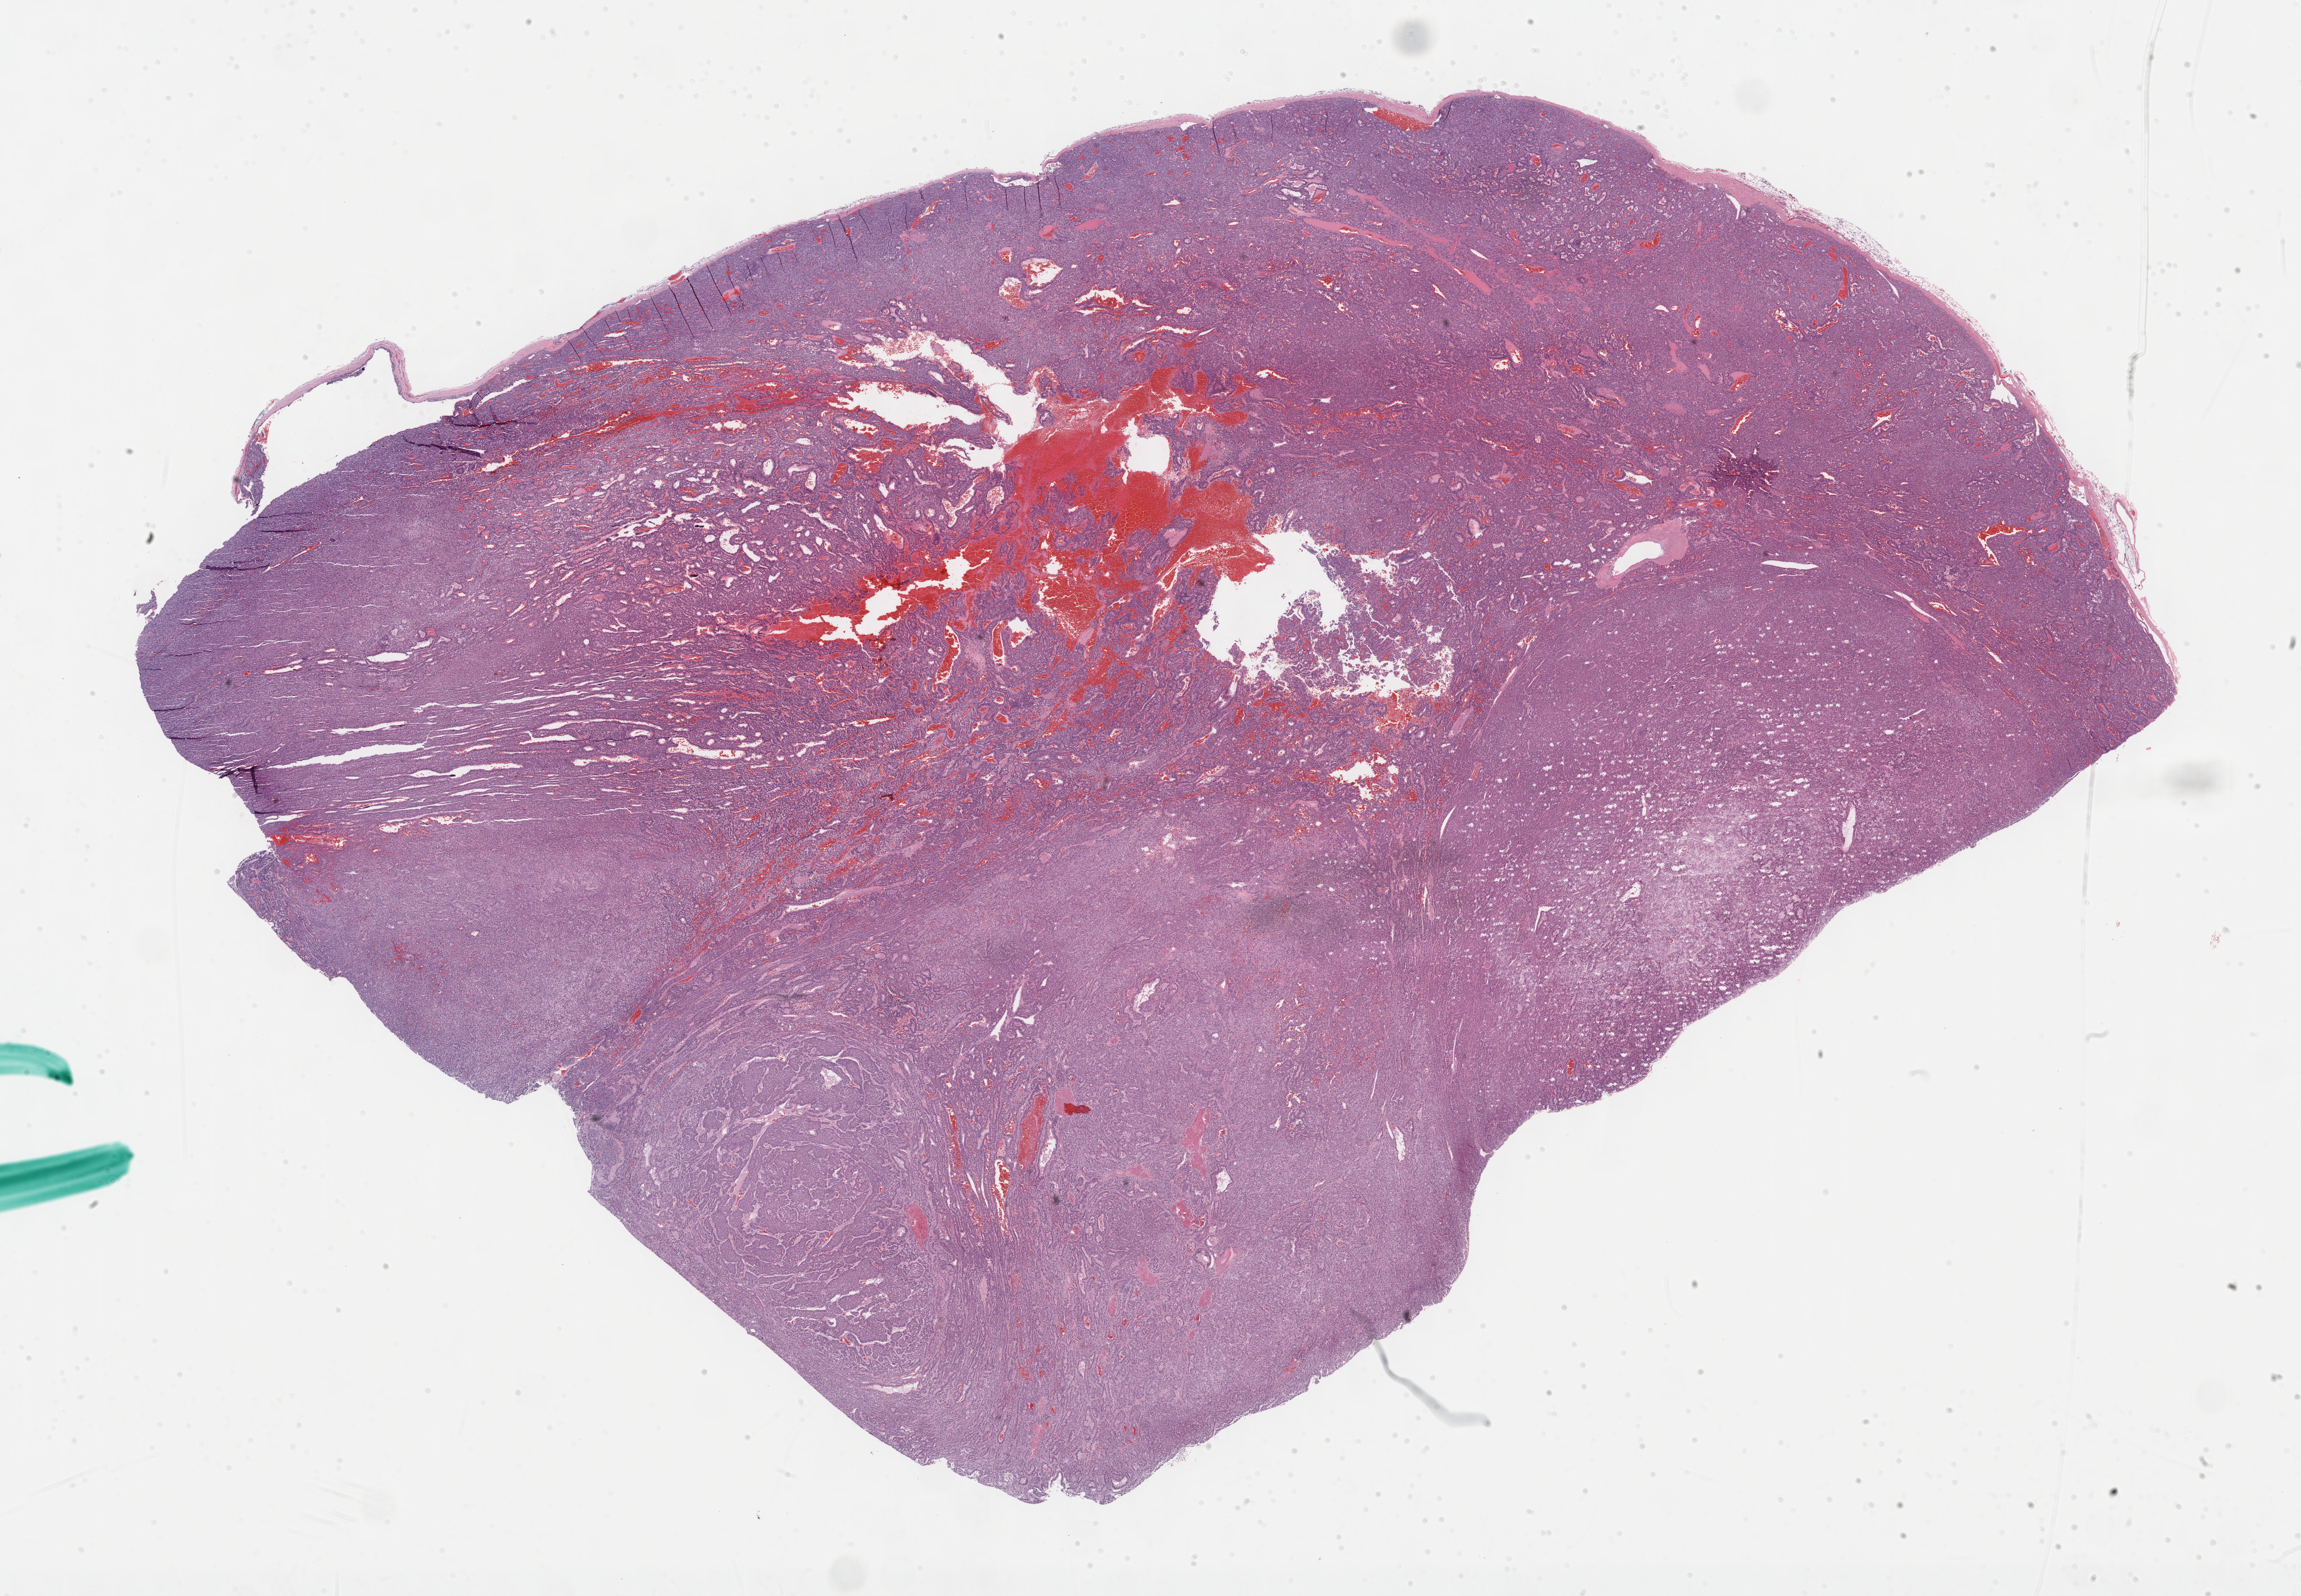
H&E-stained whole-slide image, low-resolution overview of the scanned area, about 31.2 x 21.6 mm. Formalin-fixed paraffin-embedded (FFPE) diagnostic section. Sample: primary tumour, adrenal cortex. Patient: female, age at initial diagnosis 69 years.
Histologic diagnosis: Adrenal cortical carcinoma (cortex of adrenal gland).